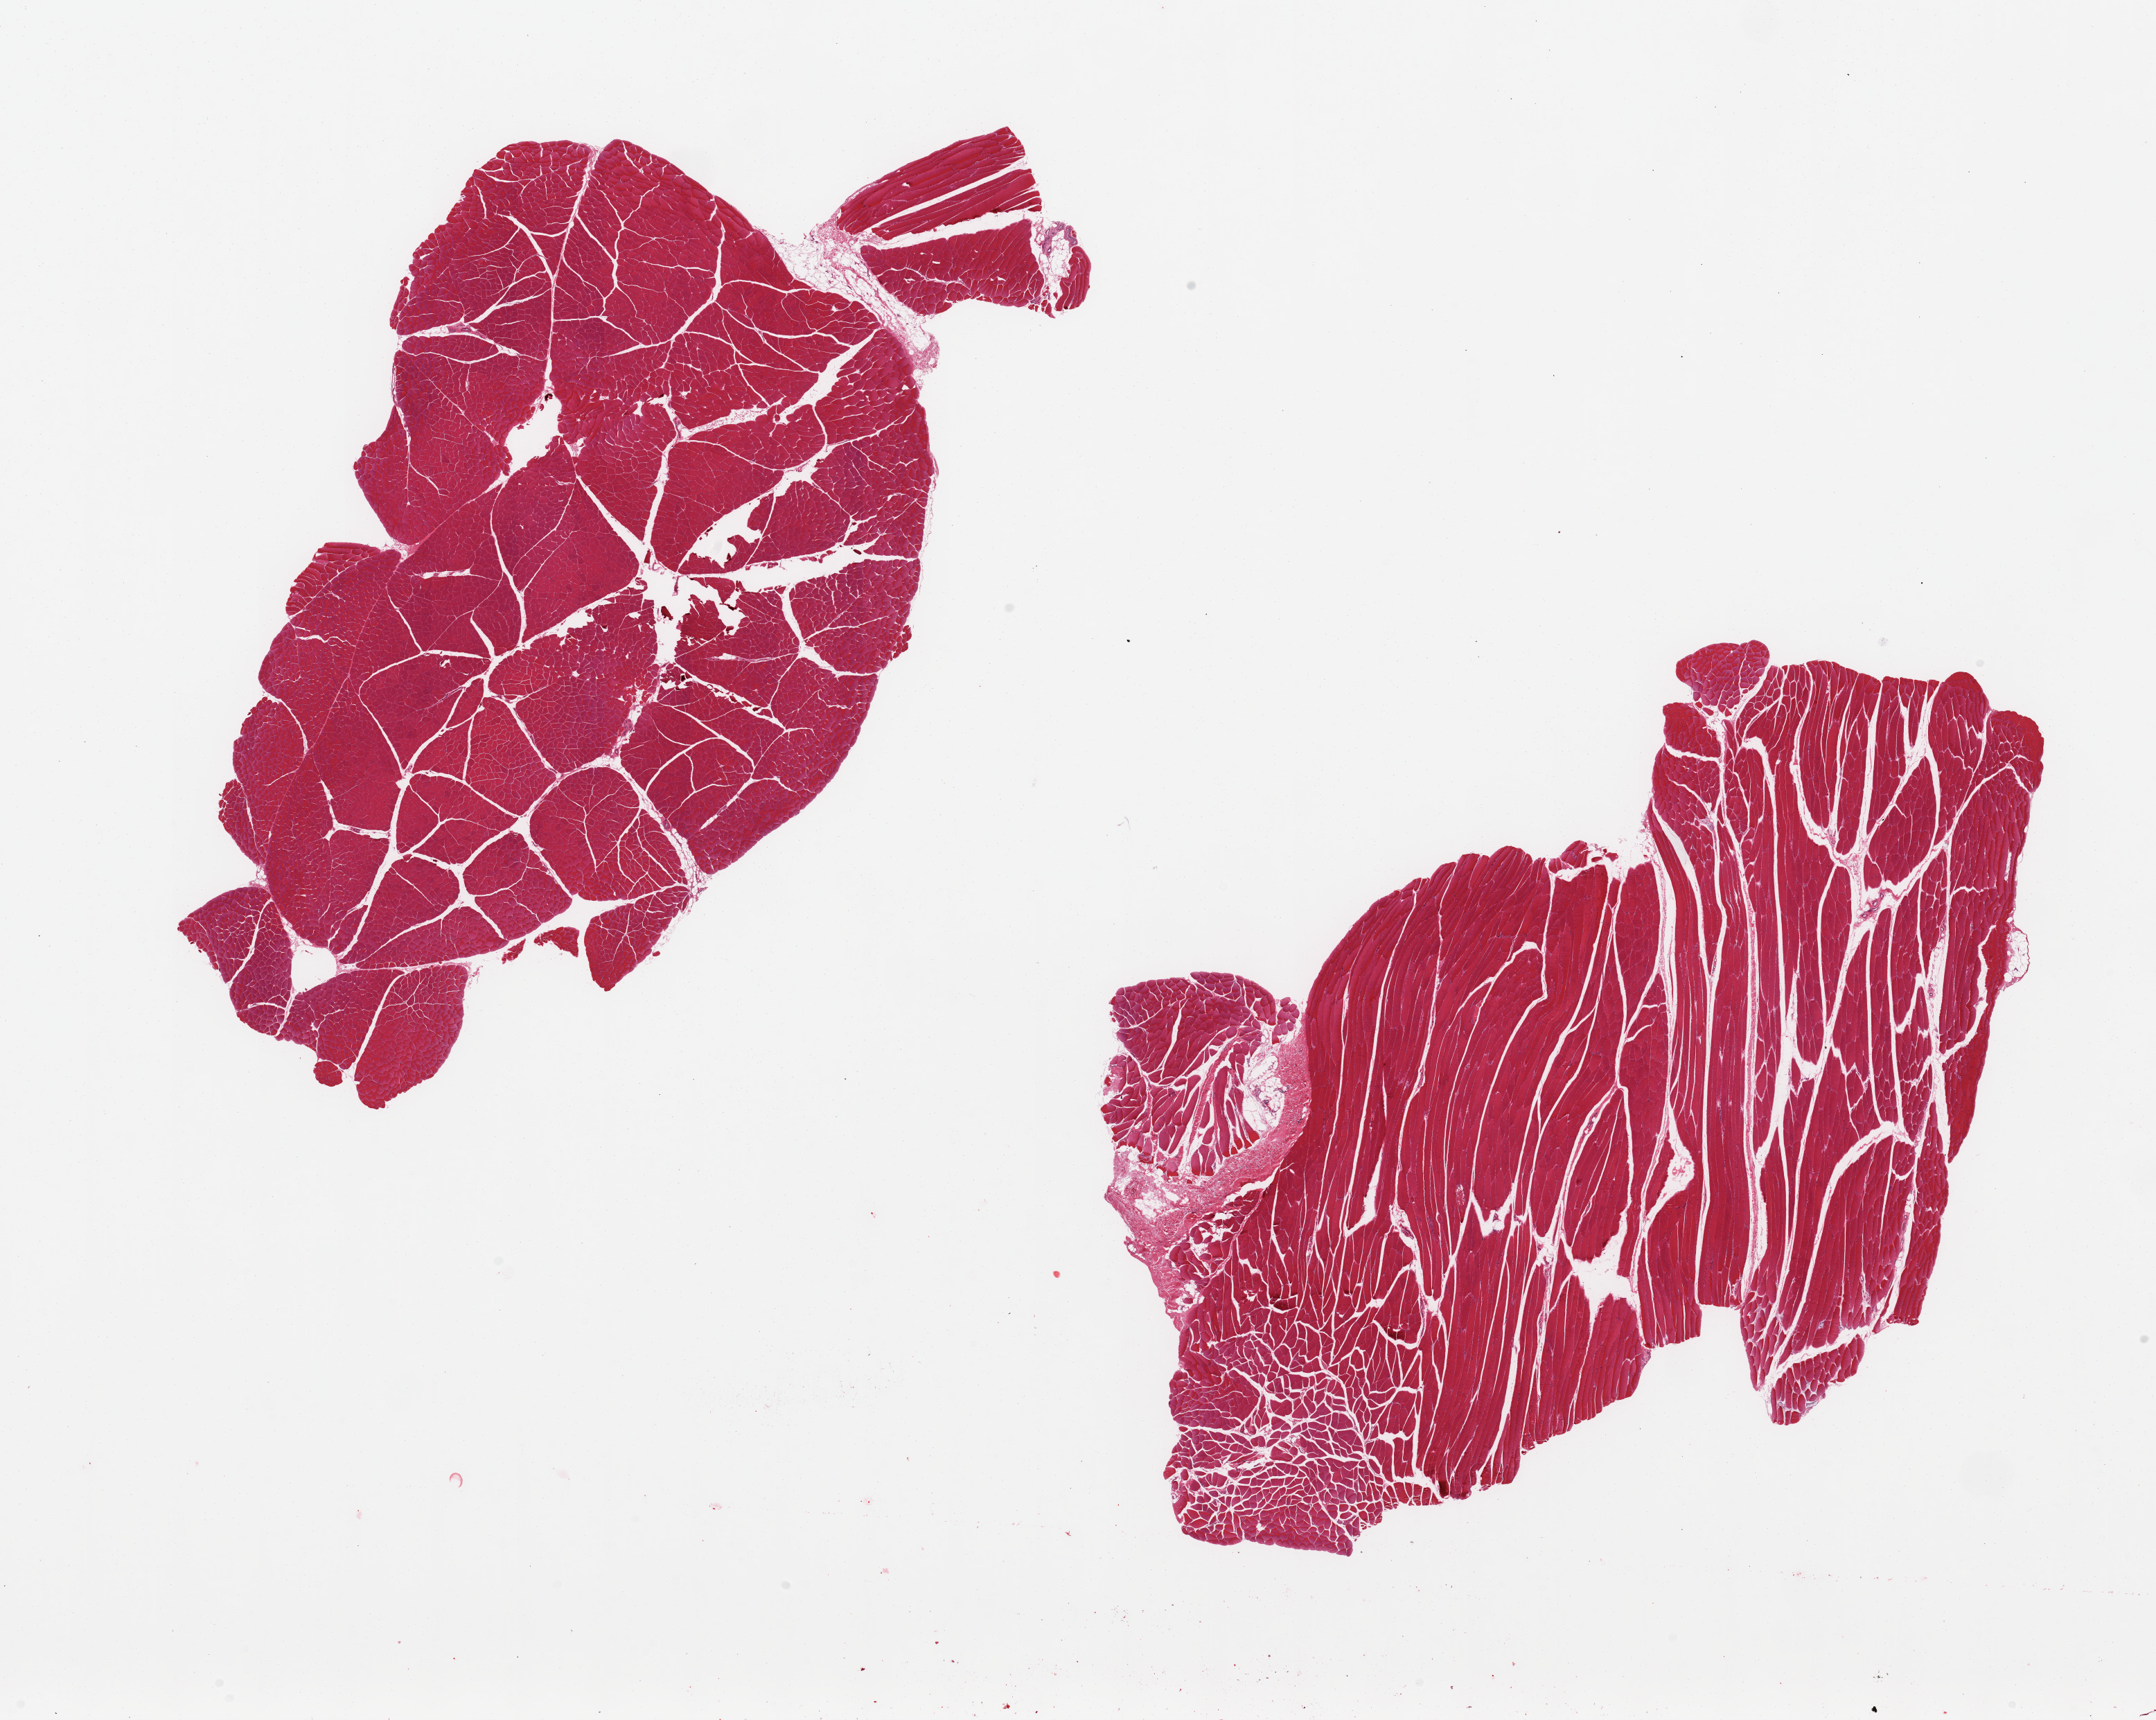
H&E whole-slide image, brightfield, whole scanned area (about 24.6 x 19.6 mm, acquisition: 20x scan) shown as a low-resolution overview, PAXgene-fixed, paraffin-embedded tissue, section of skeletal muscle (target tissue), donor tissue sample. Donor sex: male.
Reviewer comment on this tissue sample: 2 pieces; skeletal muscle with <10% fat/fibrous component.